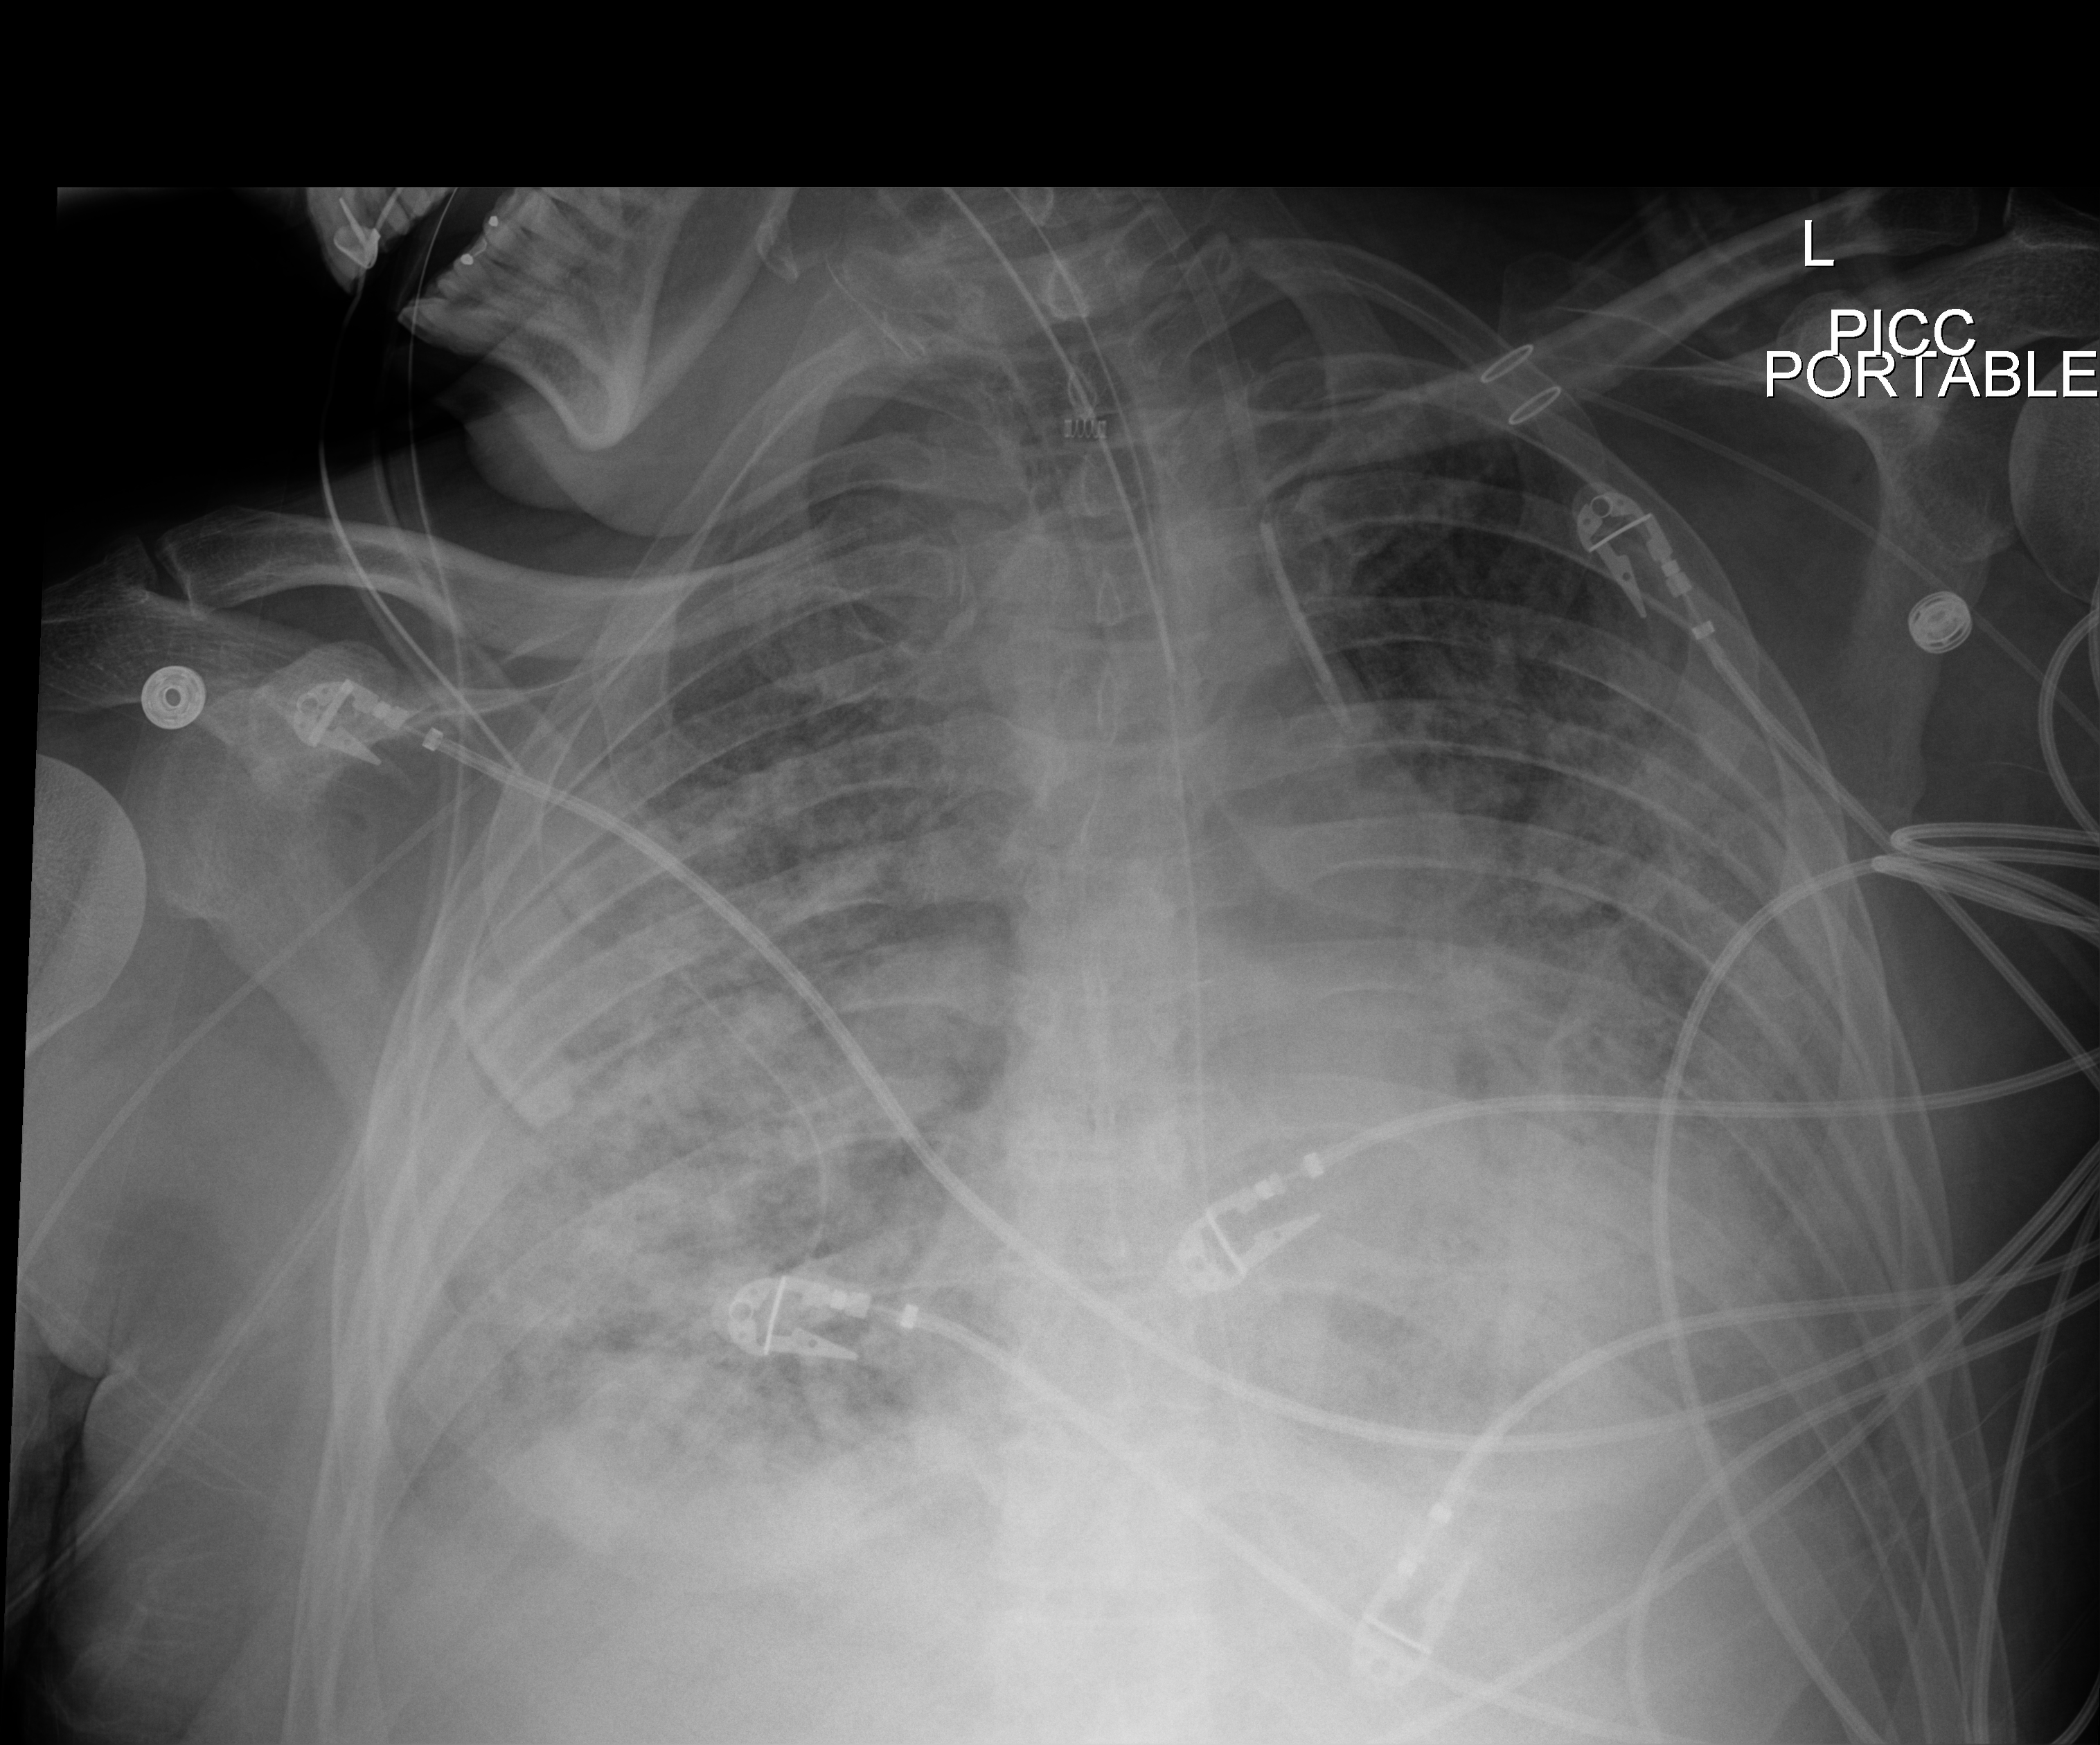
Chest X-ray (portable); anteroposterior (AP) projection. Male patient hospitalised with COVID-19, age 18–59 years.
From the hospital-stay record, not from the radiograph (when in the stay this image was taken is not recorded):
- smoking status (admission record): never
- mechanically ventilated during this hospital stay: yes